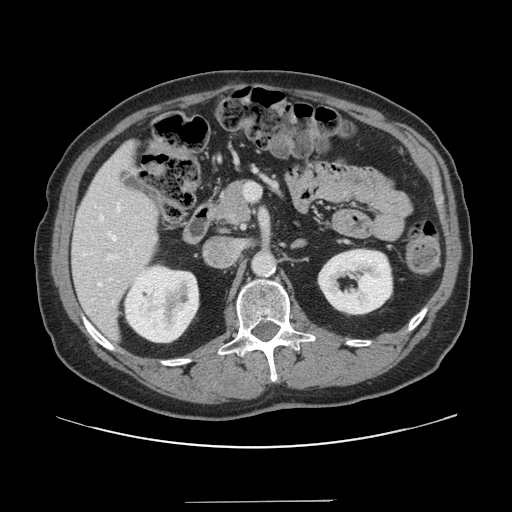
Contrast-enhanced abdominal CT, one axial slice; position 71 of 151 along the scan axis; 120 kVp; intravenous contrast given; soft-tissue window (W 400 / L 40 HU); 512 × 512 image matrix. Male patient, age 63 years. Case-level facts recorded for this patient, not image findings: diagnosis: colorectal cancer liver metastases, imaged before liver resection; multiple liver metastases: no; largest metastasis: 2.1 cm.
Structures marked on this image (outlined manually by an expert reader):
- hepatic veins: bounding box [x1, y1, x2, y2] px = [98, 206, 119, 286]
- liver: [73, 142, 158, 338]
- planned liver remnant (the part of the liver to remain after resection): [73, 143, 158, 338]
- portal vein (with intrahepatic branches): [106, 183, 259, 261]